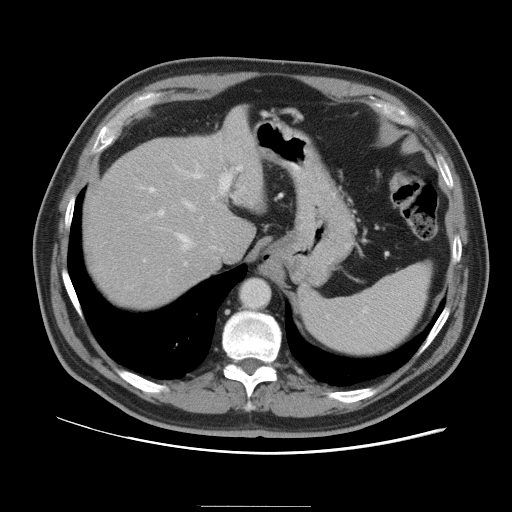
Contrast-enhanced abdominal CT, one axial slice. Position 76 of 105 along the scan axis. 120 kVp. Soft-tissue window (W 400 / L 40 HU). 5 mm slice thickness. 512 × 512 image matrix, field of view 399 × 399 mm. Male patient, age 64 years. Case-level facts recorded for this patient, not image findings: diagnosis: colorectal cancer liver metastases, imaged before liver resection; multiple liver metastases: yes; largest metastasis: 3 cm.
Annotated regions visible in this slice (manually delineated by an expert):
- hepatic veins: bounding box (x1, y1, x2, y2) in pixels: (177, 200, 195, 249)
- liver: (85, 110, 264, 309)
- planned liver remnant (the part of the liver to remain after resection): (85, 146, 237, 309)
- portal vein (with intrahepatic branches): (148, 163, 241, 265)